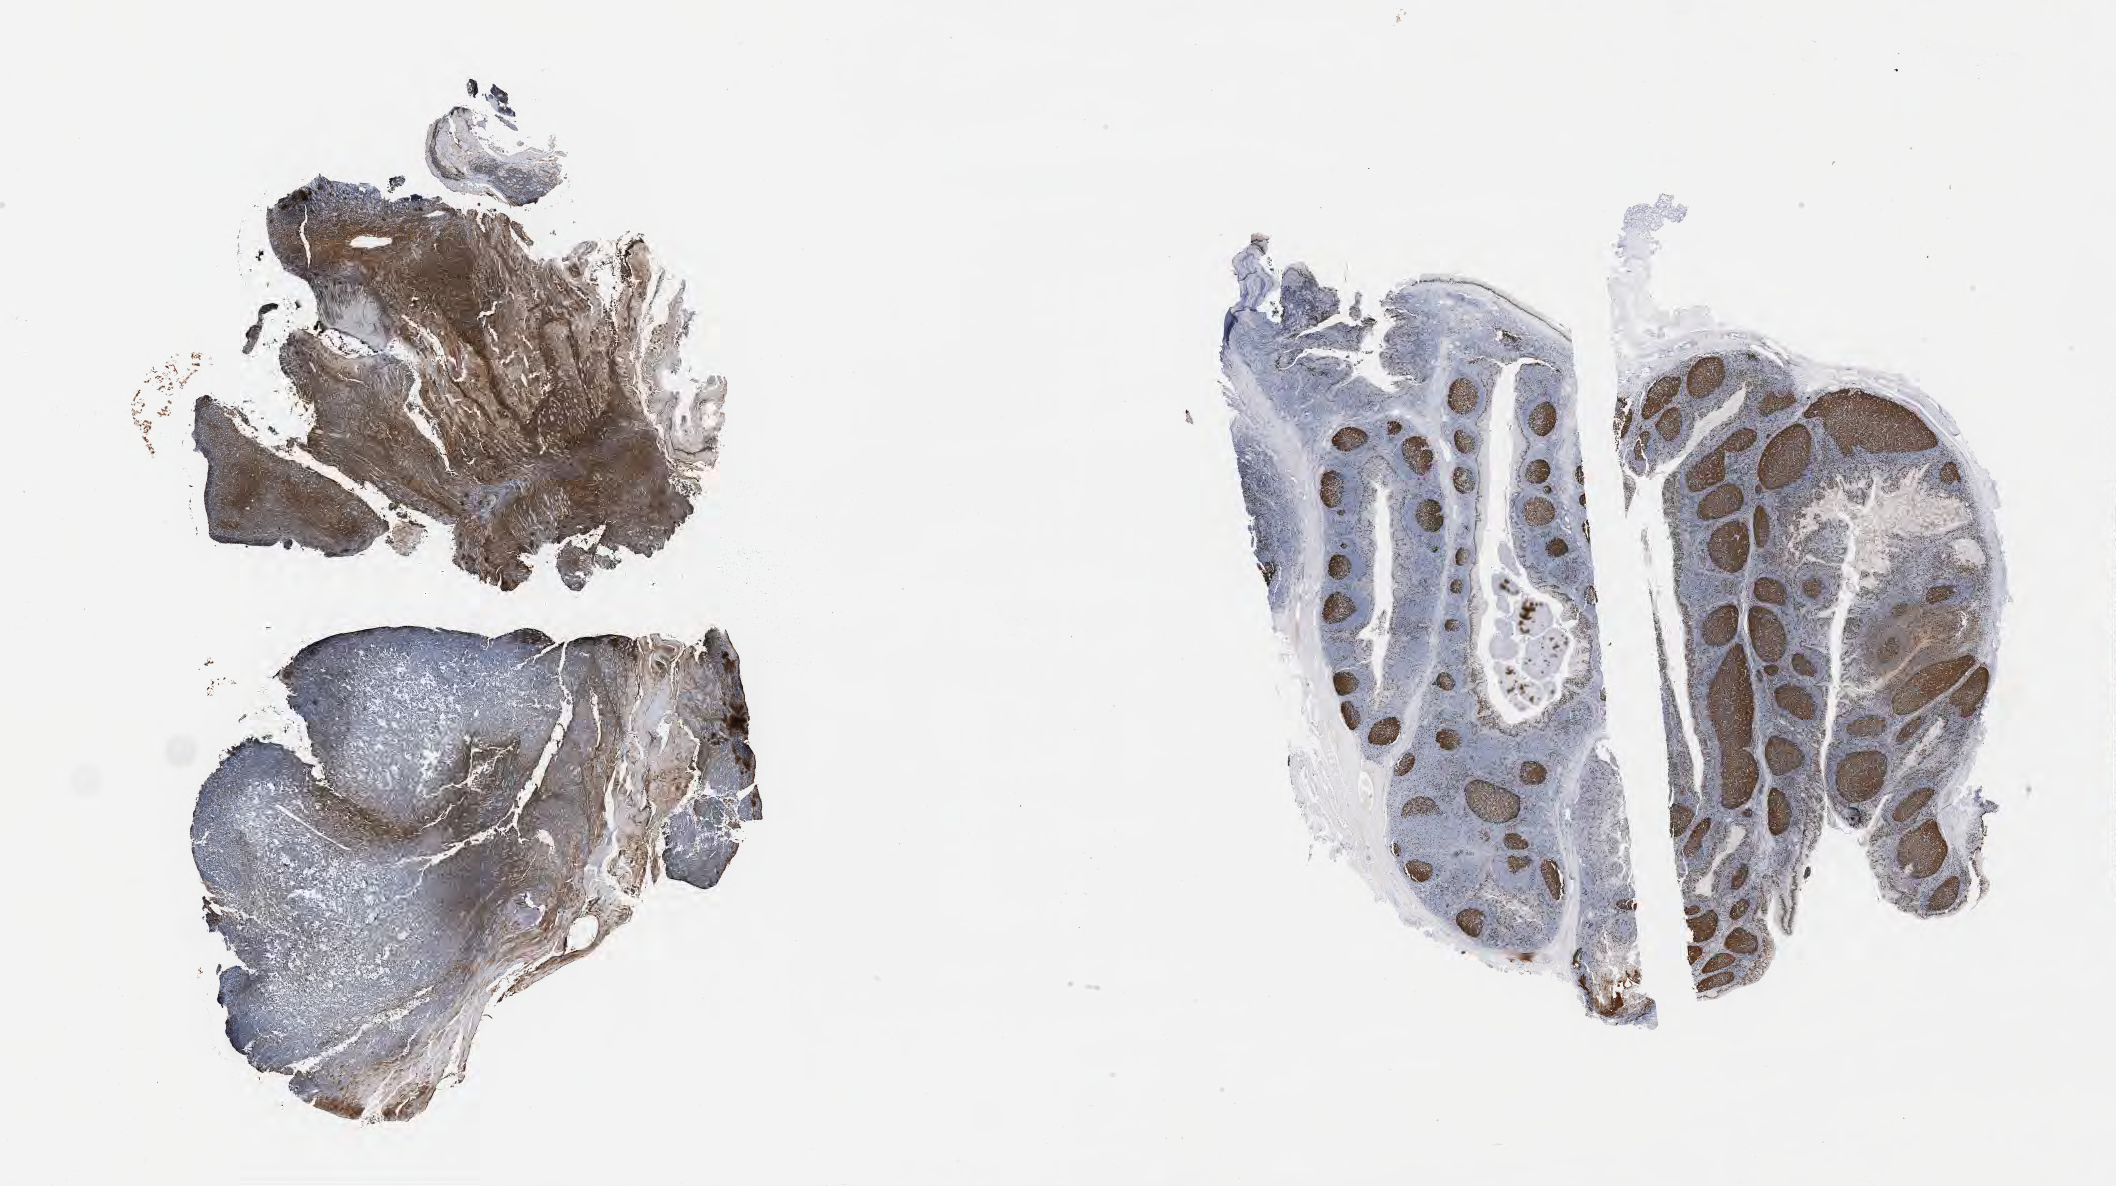
Whole-slide image, immunohistochemical stain for Ki-67, whole scanned area (about 34.2 x 19.2 mm) shown as a low-resolution overview. Specimen: tumor tissue. Patient male; aged 40.
Histologic diagnosis: Burkitt lymphoma, NOS.